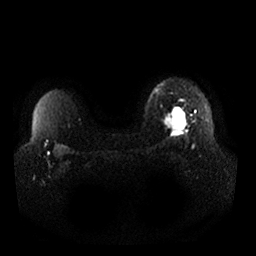
Breast MRI, one axial slice. Position 24 of 32 along the scan axis. Diffusion-weighted series; image 2 of 4 stored at this slice position (different b-values; order by instance number). 1.5 T. 4 mm slice thickness. 256 × 256 image matrix, field of view 360 × 360 mm. Female patient.
Annotated regions visible in this slice (expert manual segmentation):
- tumour on diffusion-weighted imaging: bounding box <164,108,187,131> (left, top, right, bottom; pixels)